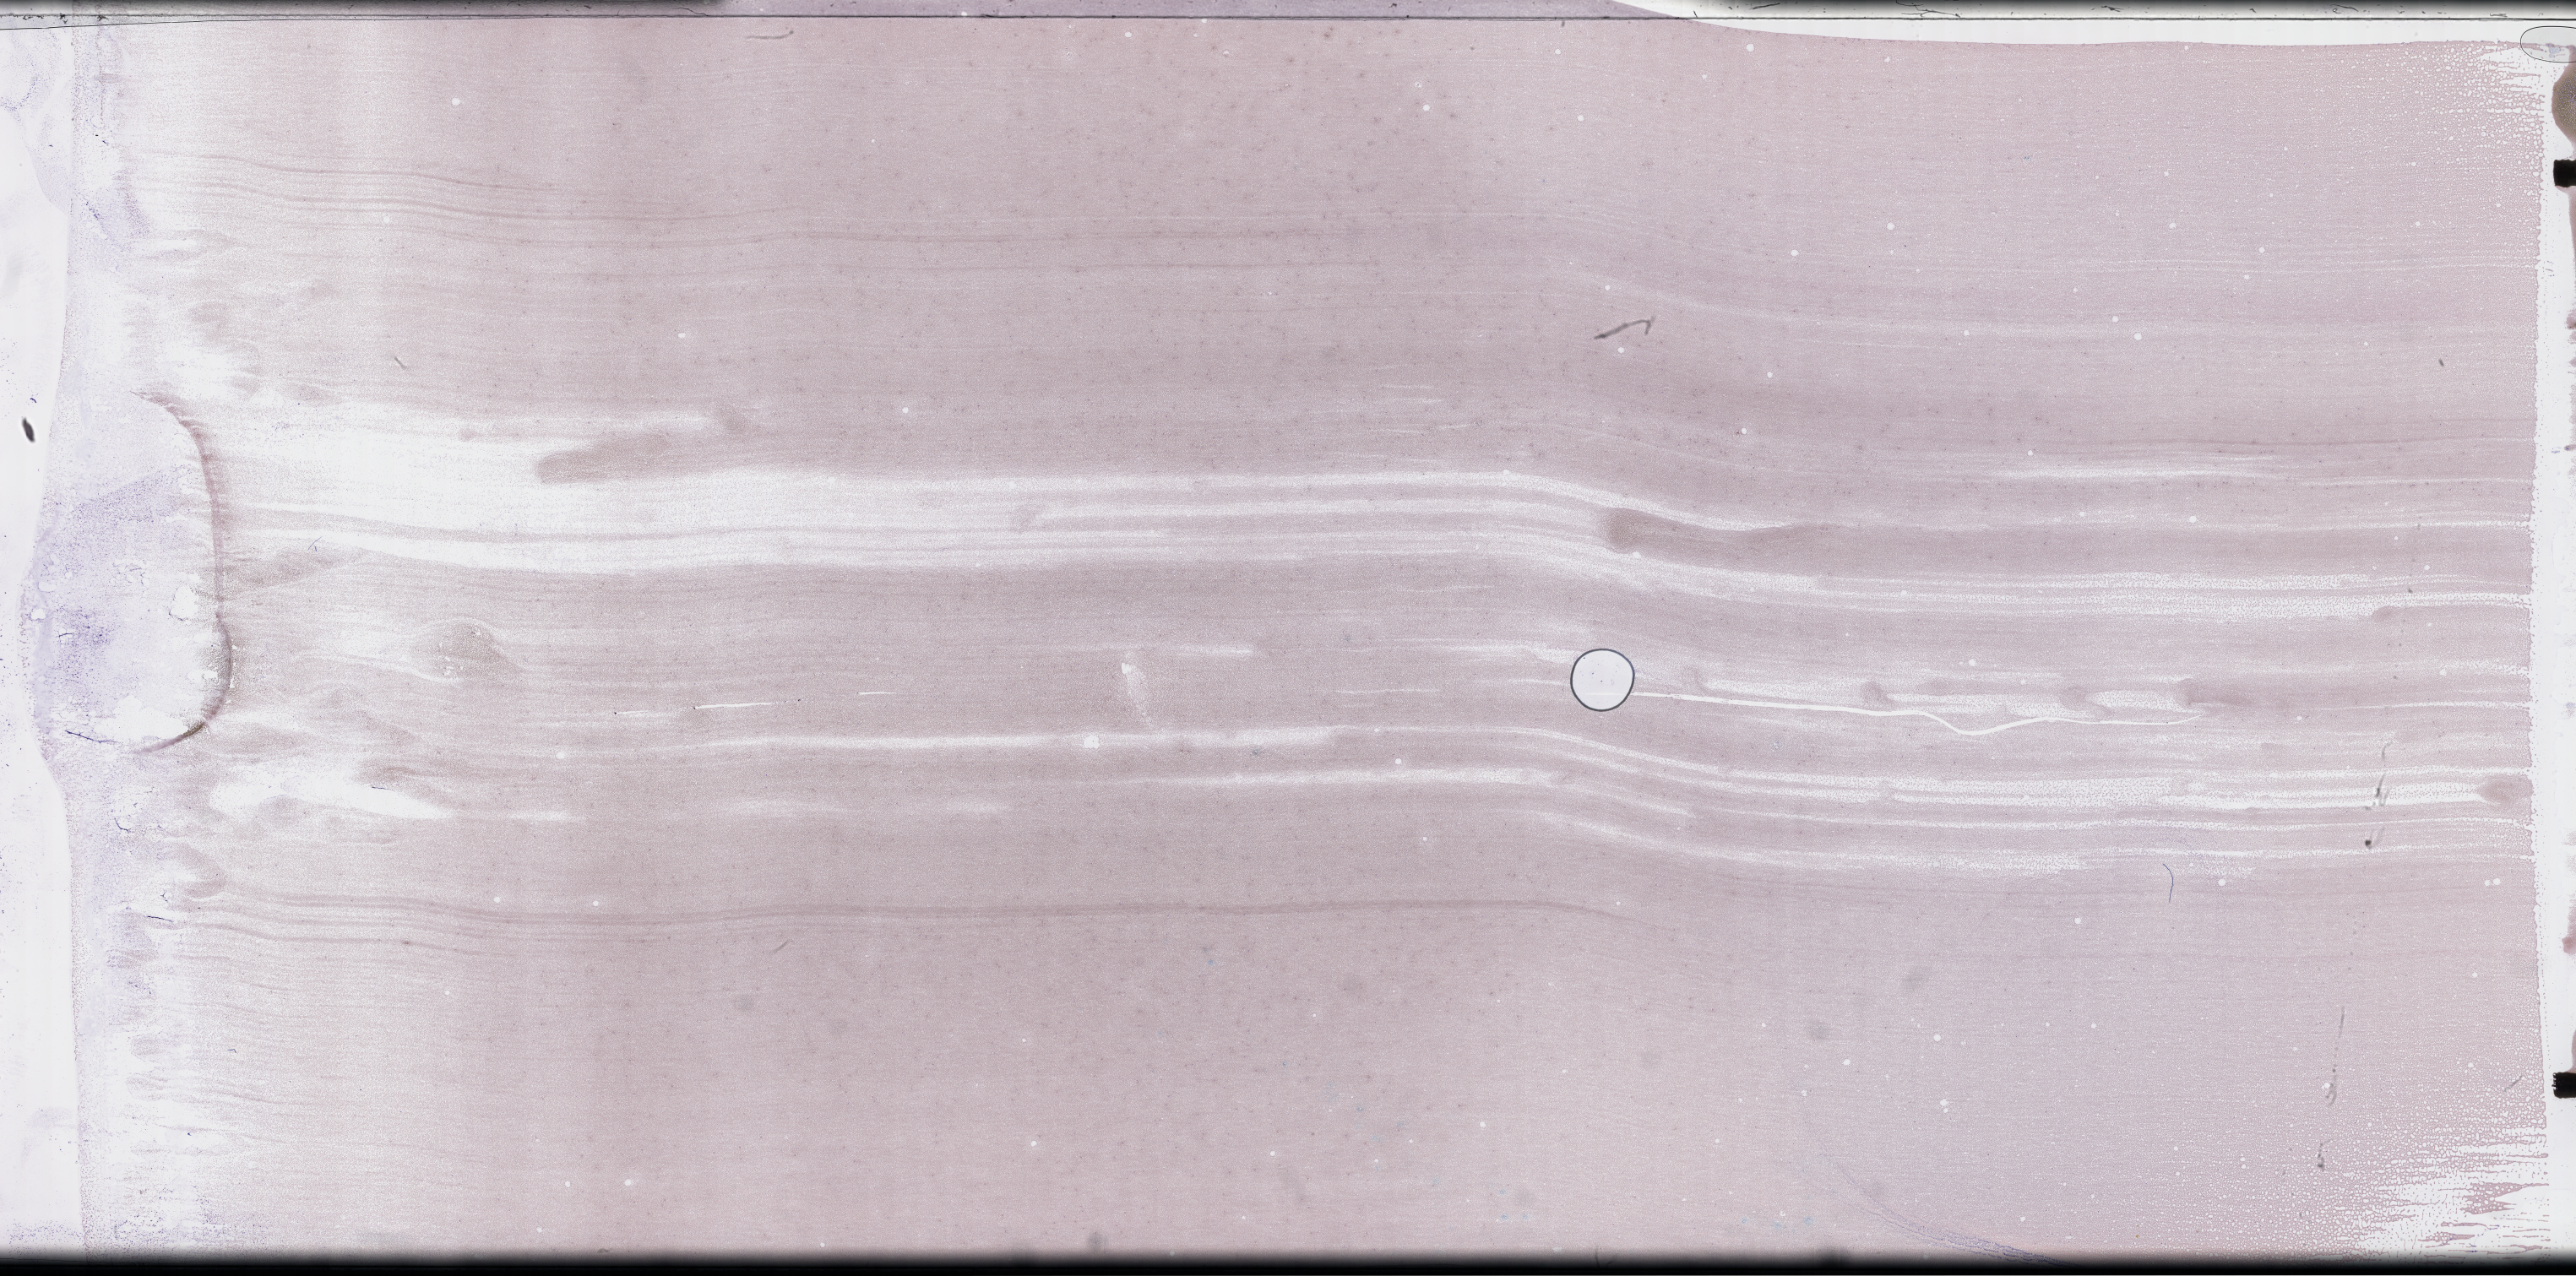
Whole-slide image of a whole blood smear, Wright–Giemsa stain, whole scanned area (about 49.3 x 24.4 mm) shown as a low-resolution overview. Smear from an EDTA sample. Collected on treatment. Patient sex: male.
Patient diagnosis: Plasma Cell Myeloma.